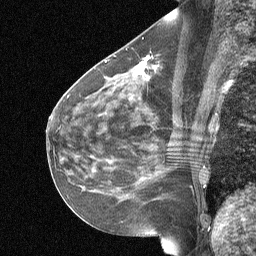
Breast MRI (dynamic contrast-enhanced), one sagittal slice; slice 32 of 64 in the series (ordered by position); dynamic contrast-enhanced study with each time point stored as its own series, time point 2 of 3 at this slice position (early post-contrast, ordered by acquisition time); 1.5 T; TE 4.8 ms, TR 27 ms; 2 mm slice thickness; 256 × 256 image matrix, field of view 200 × 200 mm. Female patient, age 51 years. From the clinical record (not read from this slice): setting: breast cancer imaged before/during neoadjuvant chemotherapy; receptor status: HR-positive, HER2-negative.
Annotated regions visible in this slice (semi-automatic segmentation, software-assisted and operator-edited):
- analysis volume of interest (the breast-tissue region the enhancement analysis was run in; not a lesion): bounding box [x1, y1, x2, y2] px = [88, 42, 186, 119]
- tumour enhancement mask (voxels above the 90 % enhancement threshold inside the analysis volume of interest): [136, 57, 149, 74]